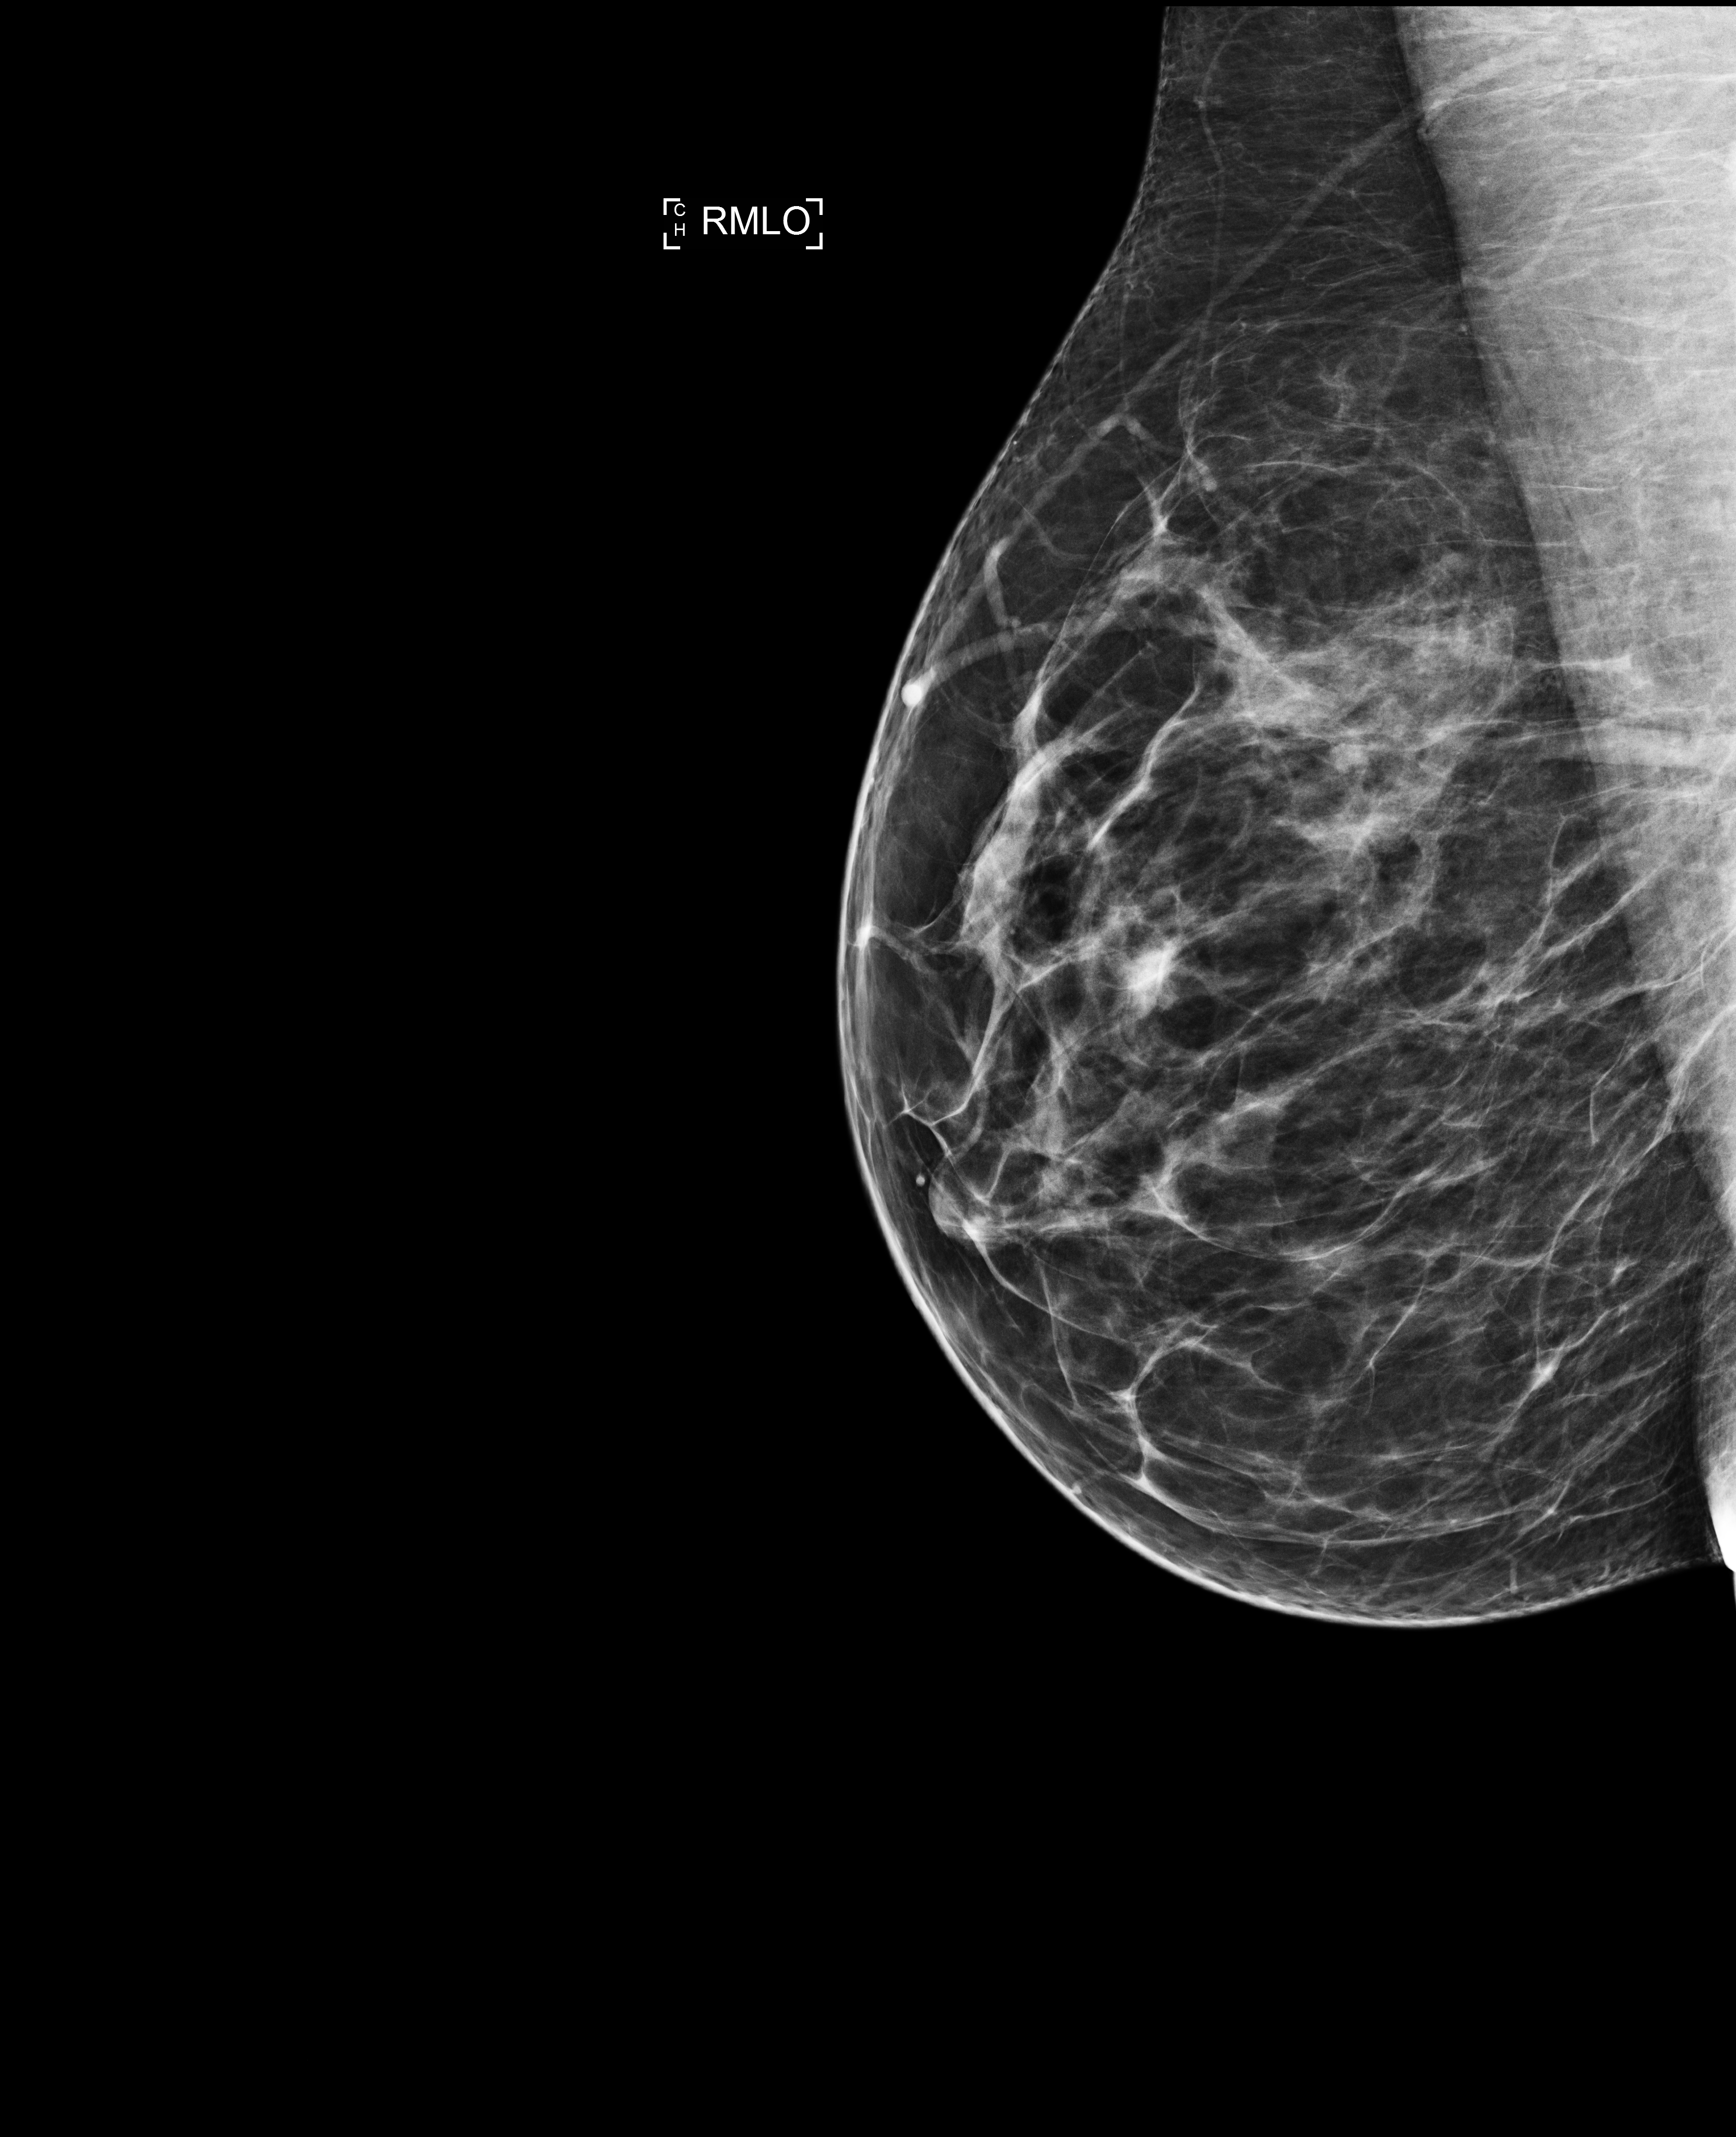
Full-field digital mammogram (FFDM); right breast; MLO view; screening examination; compressed breast thickness 71 mm. Female patient, age 40 years.
Breast density at the screening exam (both breasts): scattered fibroglandular densities (BI-RADS density category b). Final BI-RADS category for the screening round (tomosynthesis exam, both breasts): category 1. Recall: no recall after this screen.